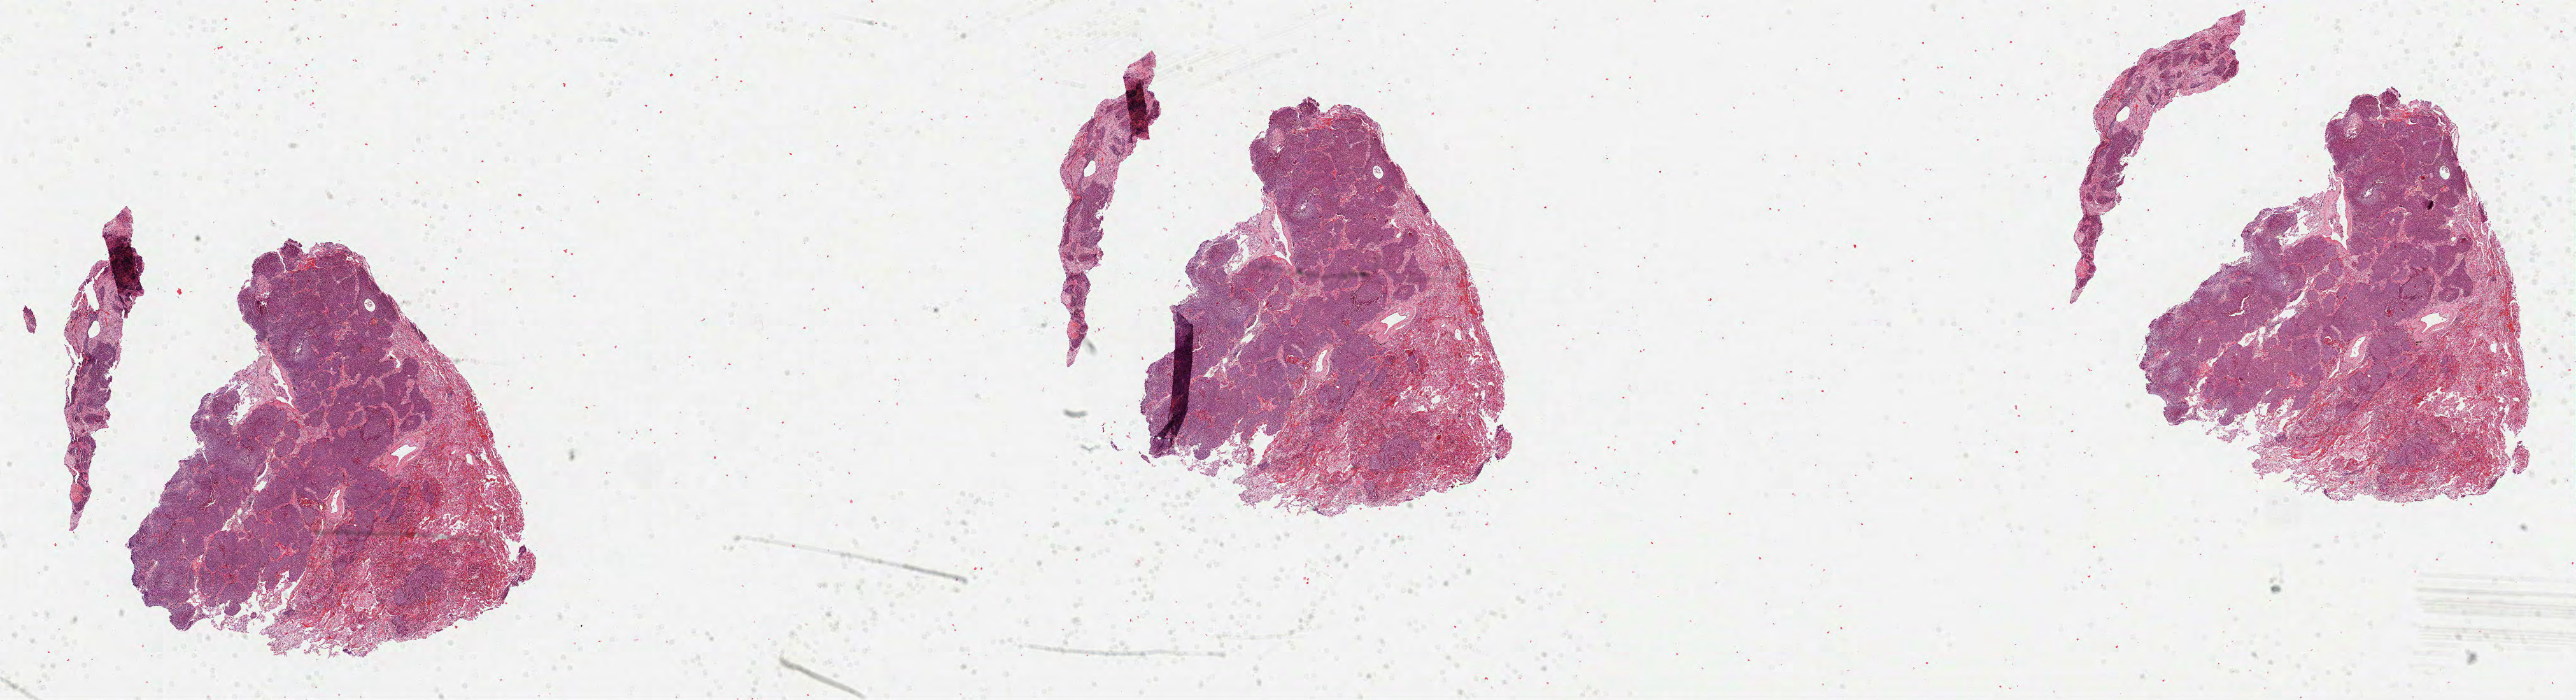
H&E-stained whole-slide image, low-resolution overview of the scanned area, about 32.6 x 8.9 mm (acquisition: 40x scan). Formalin-fixed paraffin-embedded (FFPE) diagnostic section. Primary tumour sample from the lung. Patient: male, age at initial diagnosis 58 years.
AJCC pathologic stage: IIIA. Histologic diagnosis: Squamous cell carcinoma, NOS. Laterality: left.